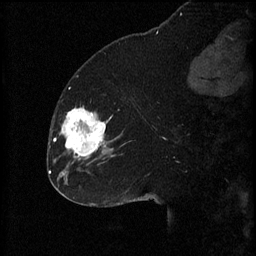
Breast MRI (dynamic contrast-enhanced), one sagittal slice. Slice 25 of 60 in the series (ordered by position). 3 images stored at this slice position (order not interpretable as contrast timing). 1.5 T. TE 4.2 ms, TR 8.2 ms. 2 mm slice thickness. 256 × 256 image matrix, field of view 180 × 180 mm. Female patient, age 32 years.
Structures marked on this image (semi-automatic segmentation, software-assisted and operator-edited):
- analysis volume of interest (the breast-tissue region the enhancement analysis was run in; not a lesion): box from (x=59, y=106) to (x=111, y=165) px
- tumour enhancement mask (voxels above the 70 % enhancement threshold inside the analysis volume of interest): (x=61, y=106)–(x=106, y=157)